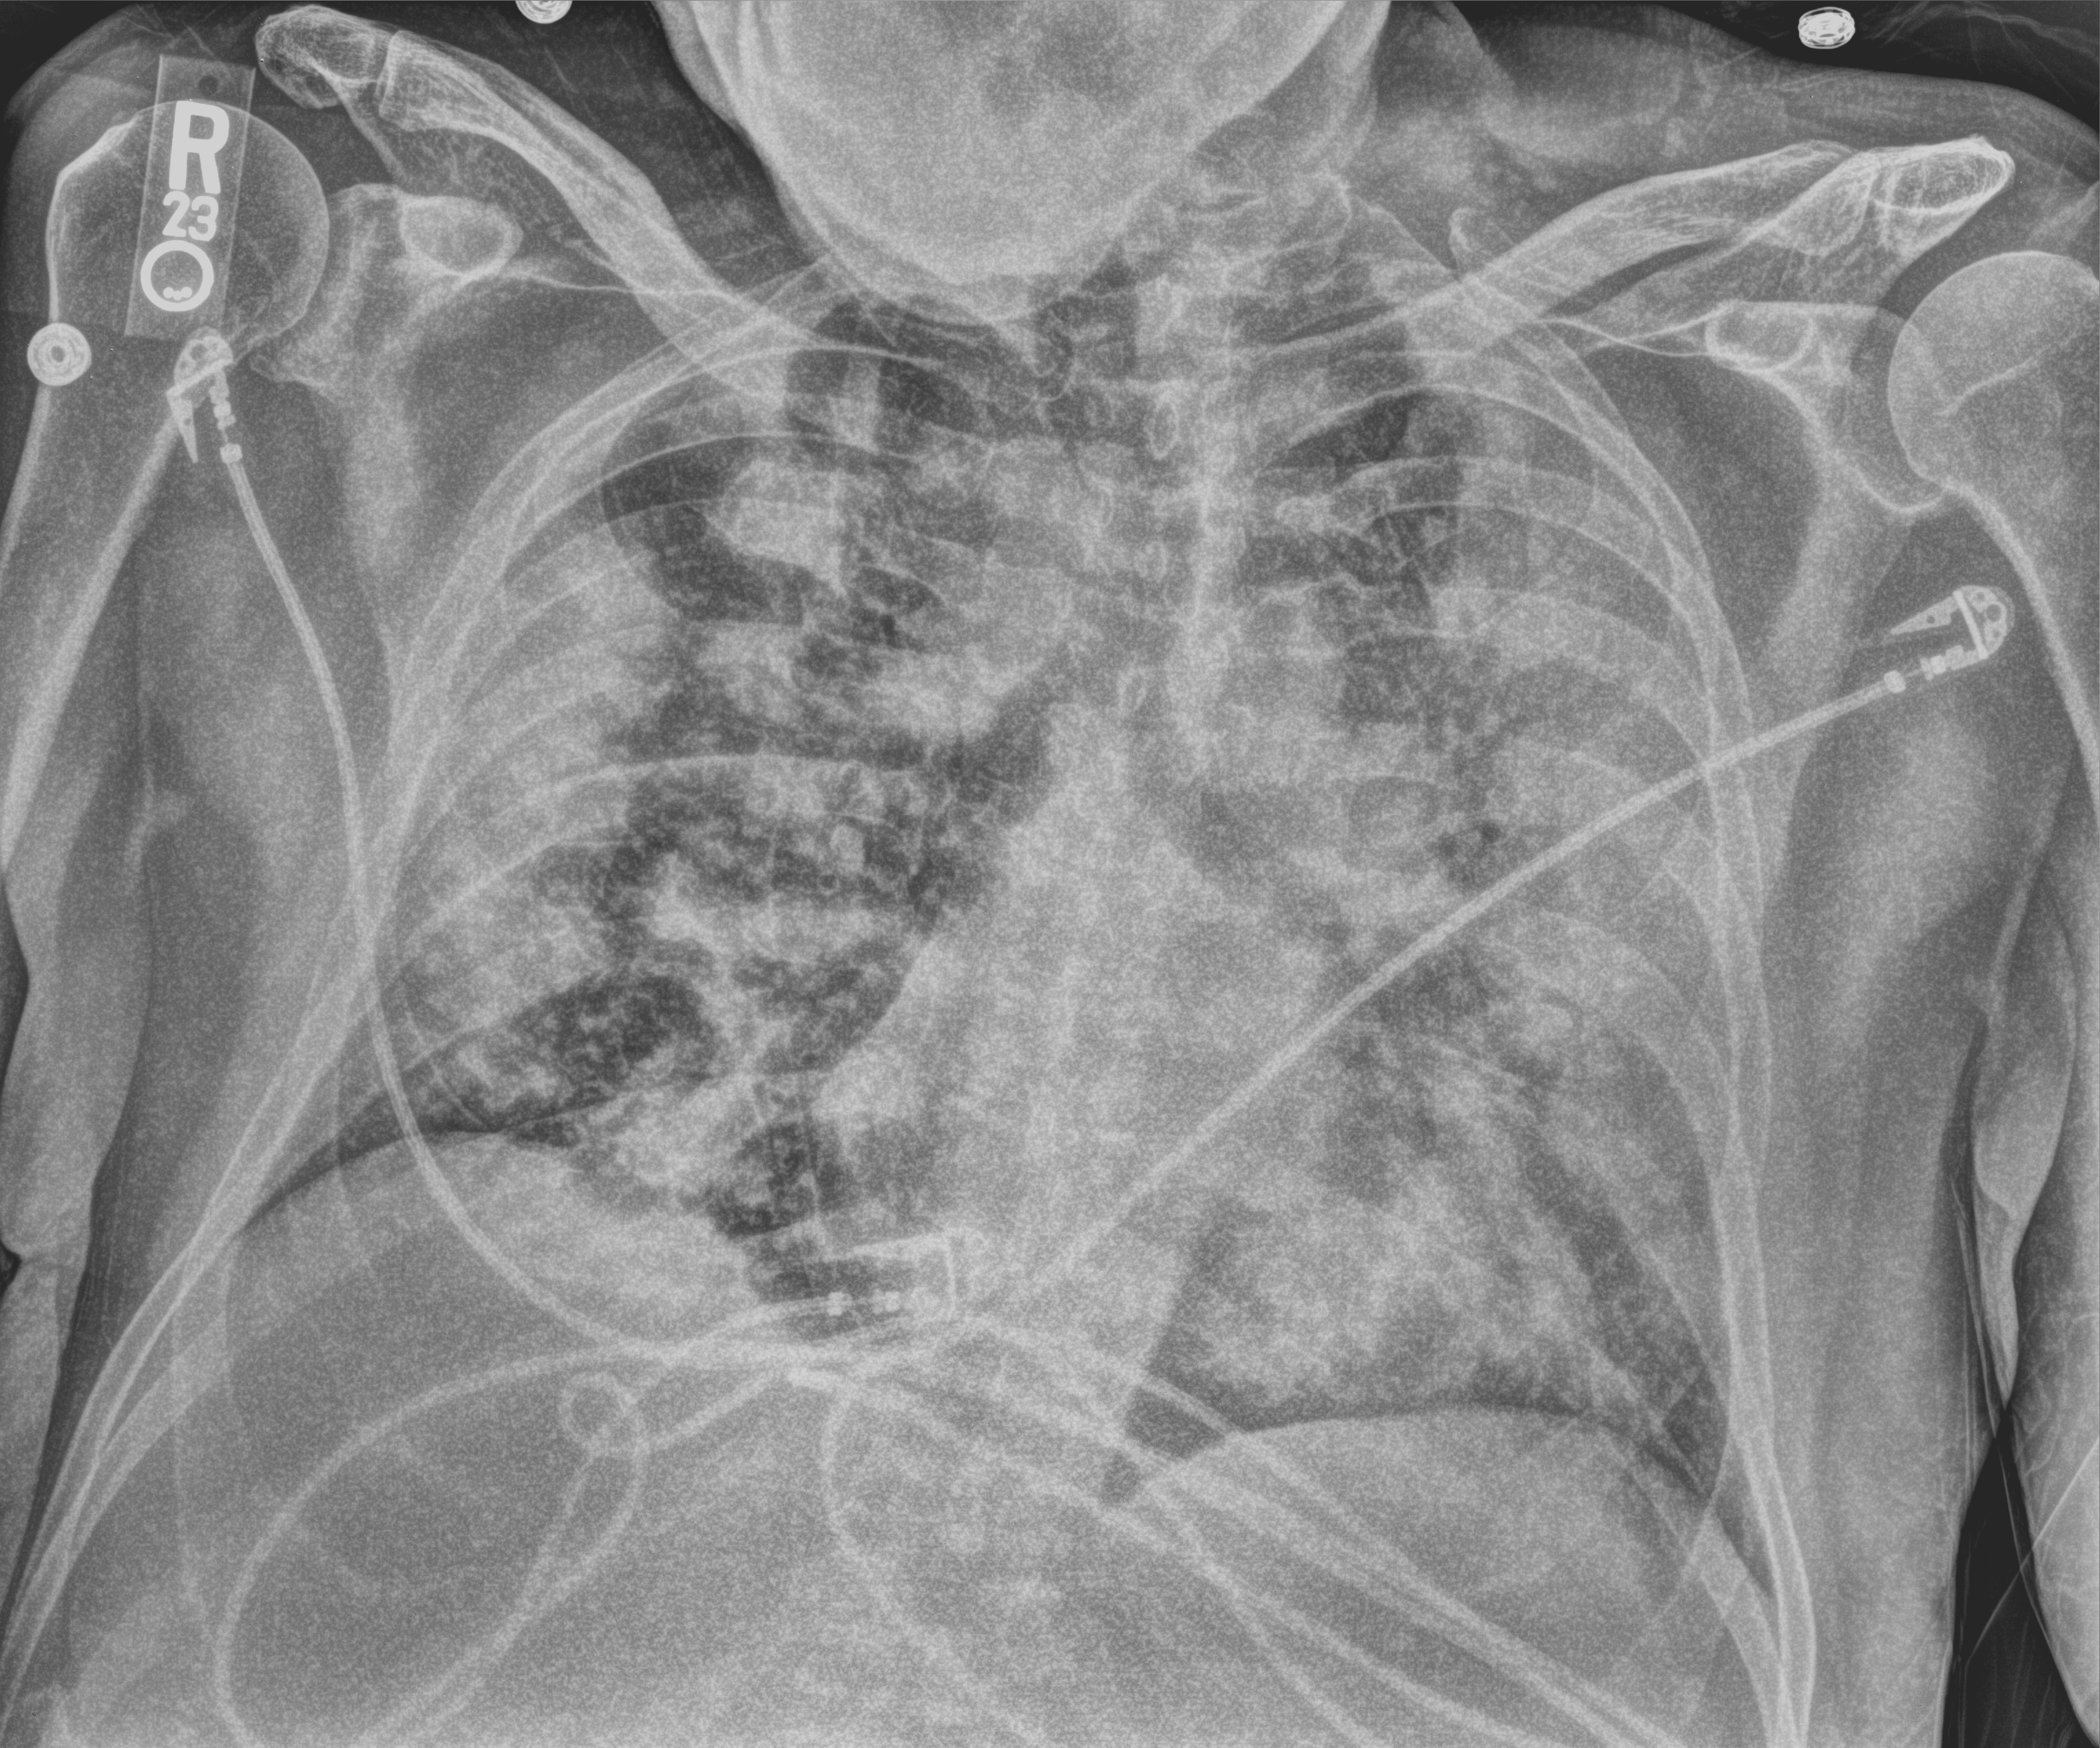
Bedside chest radiograph (computed radiography); anteroposterior (AP) projection. Male patient hospitalised with COVID-19, age 18–59 years.
From the hospital-stay record, not from the radiograph (when in the stay this image was taken is not recorded): admitted to intensive care during this hospital stay: yes; chronic kidney disease (admission record): no; mechanically ventilated during this hospital stay: yes.